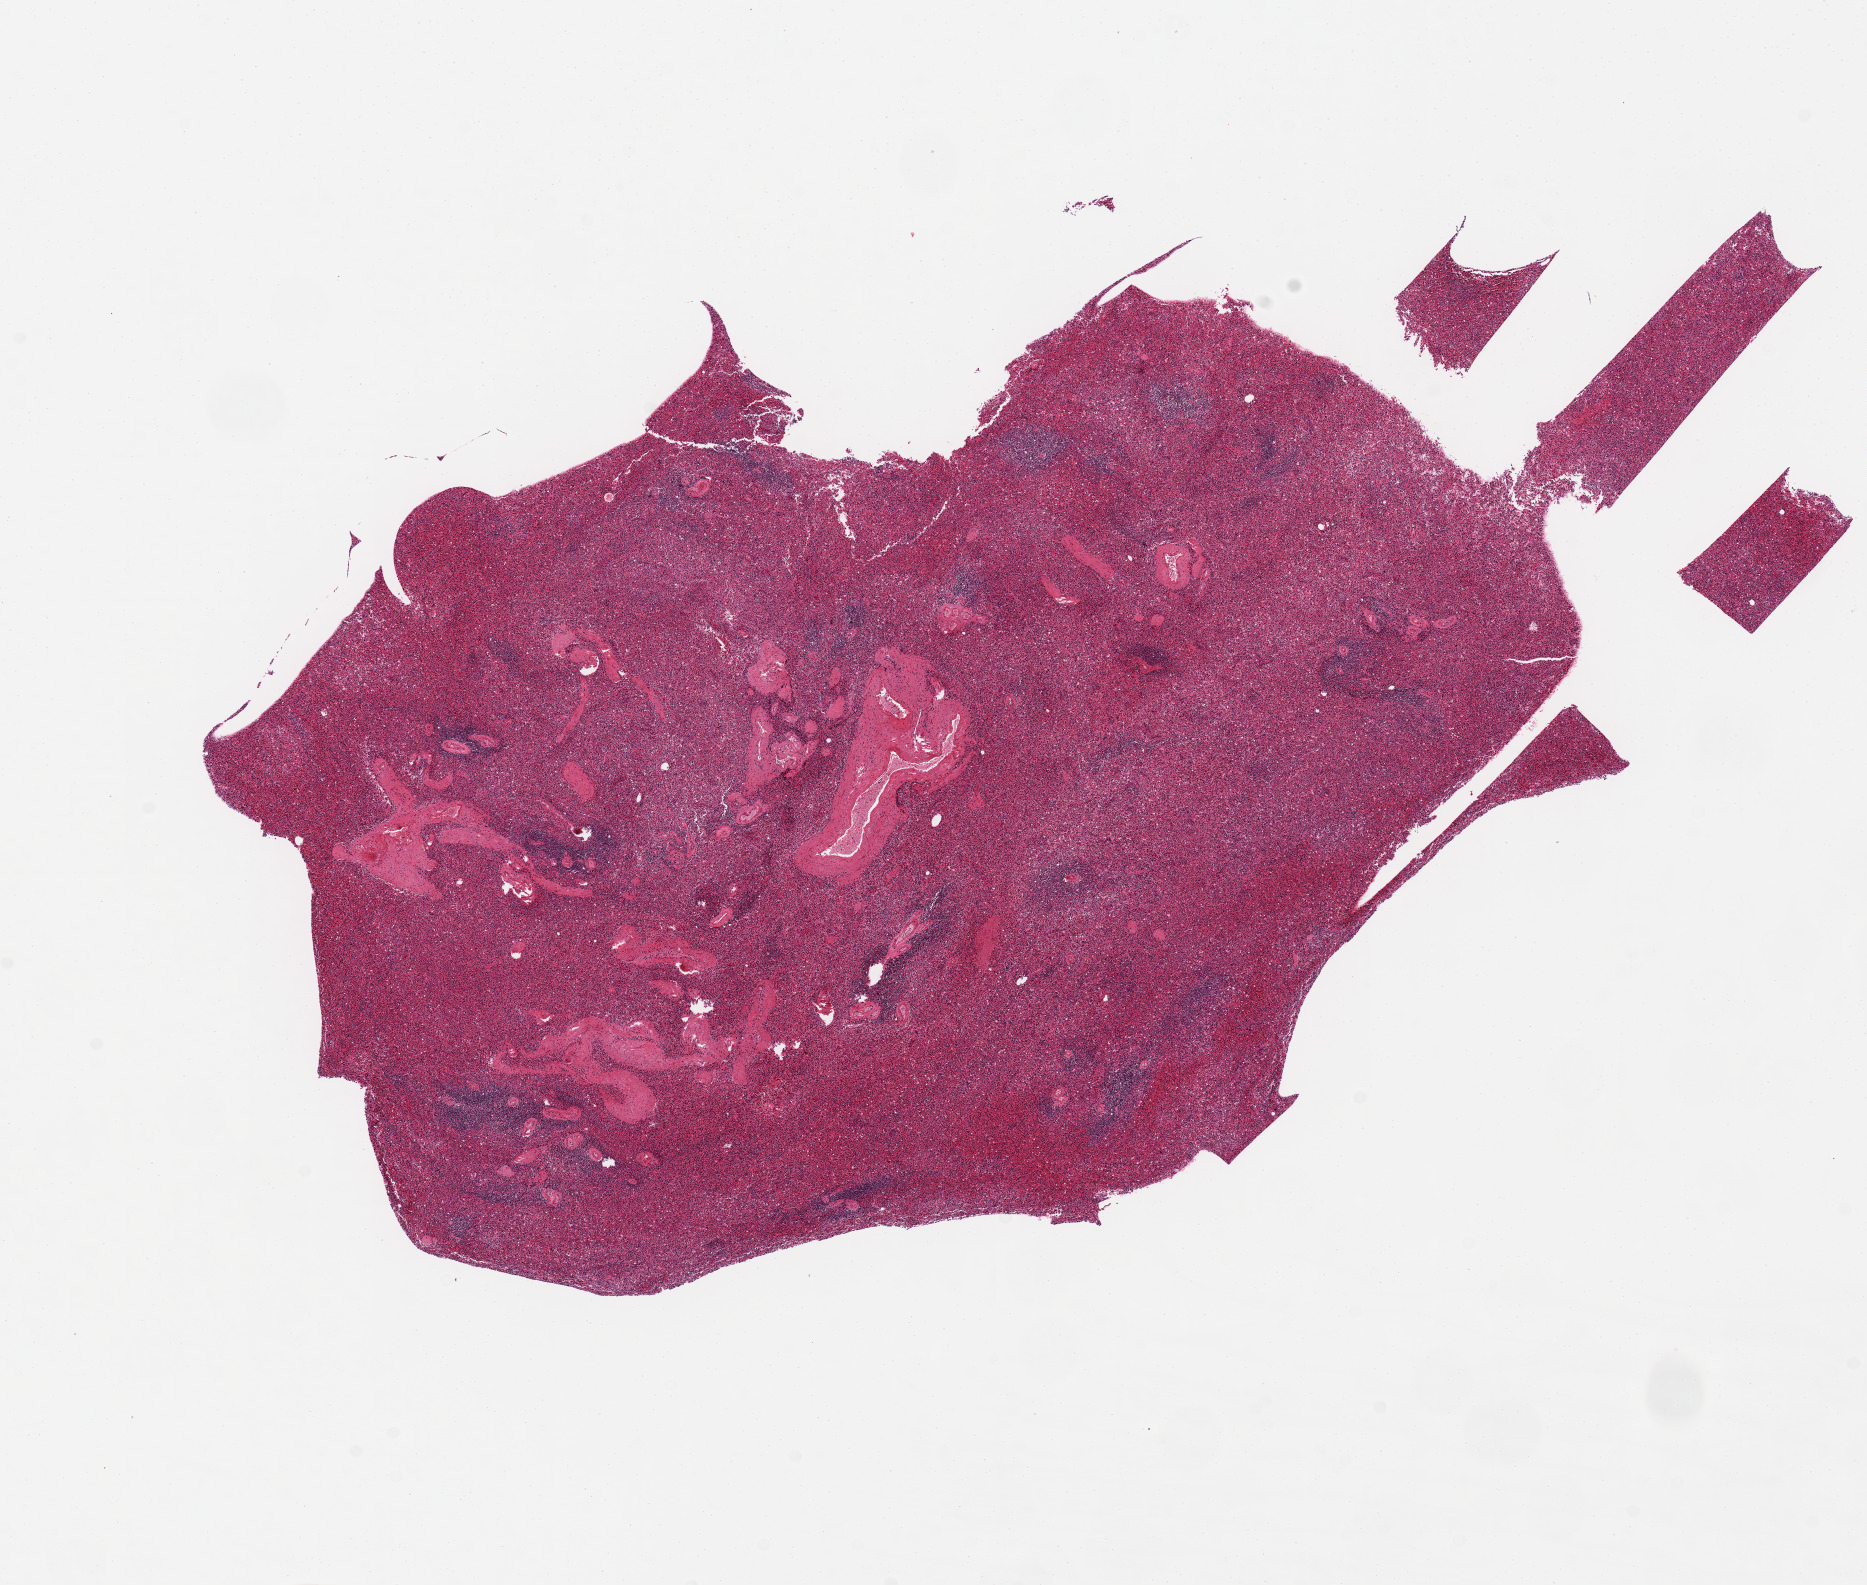
Digitized hematoxylin and eosin (H&E)-stained section — a low-resolution overview of the entire scanned area, about 14.8 x 12.5 mm (from a 20x scan), PAXgene-fixed, paraffin-embedded tissue, sampled site (target tissue): spleen, donor tissue sample. Female donor.
Pathologist's review note for this sample: 10x7.5mm. Cassette grid marks.